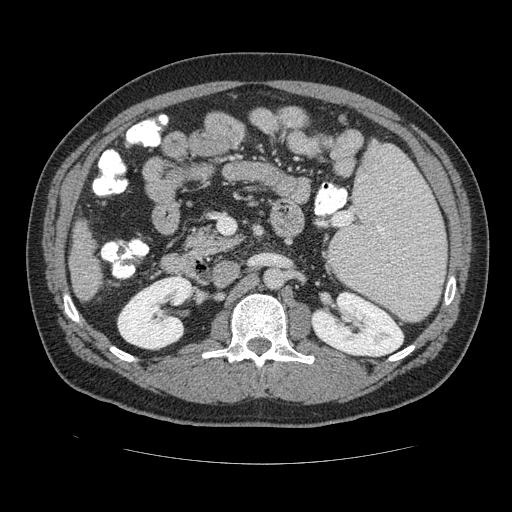
Contrast-enhanced abdominal CT (liver protocol), one axial slice. Slice 52 of 113 in the series (ordered by position). Reconstruction kernel STANDARD. Soft-tissue window (W 400 / L 40 HU). 512 × 512 image matrix, field of view 400 × 400 mm. From the clinical record (not read from this slice): diagnosis: hepatocellular carcinoma (patient treated with transarterial chemoembolisation; whether this scan precedes or follows treatment is not stated here); TNM stage (as recorded): Stage-II; Child-Pugh class: B; tumour nodularity: multinodular; tumour size: 4.8 cm.
Outlined on this slice (semi-automatically segmented with operator editing):
- liver parenchyma outside the tumour (the mass and vessels are separate outlines, so this box may not span the whole liver): bounding box <66,214,104,304> (left, top, right, bottom; pixels)